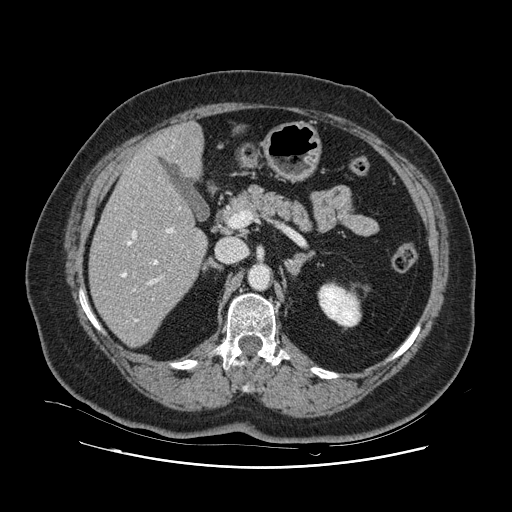
Contrast-enhanced abdominal CT, one axial slice; slice 55 of 132 in the series (ordered by position); intravenous contrast given; soft-tissue window (W 400 / L 40 HU); 2.5 mm slice thickness; 512 × 512 image matrix. Female patient, age 73 years. From the clinical record (not read from this slice): diagnosis: colorectal cancer liver metastases, imaged before liver resection; multiple liver metastases: no; largest metastasis: 7 cm; chemotherapy before resection: yes.
Structures marked on this image (outlined manually by an expert reader):
- hepatic veins: bounding box <122,146,181,322> (left, top, right, bottom; pixels)
- liver: <90,123,206,346>
- planned liver remnant (the part of the liver to remain after resection): <90,148,206,346>
- portal vein (with intrahepatic branches): <134,228,174,290>